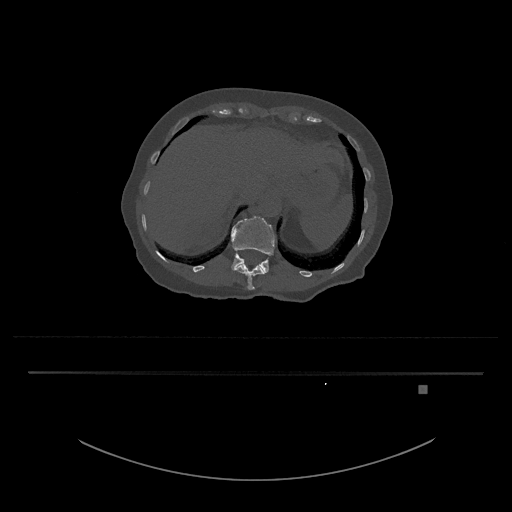
CT including the spine, one axial slice; position 582 of 797 along the scan axis; reconstruction kernel Br40s/3; 120 kVp; bone window (W 1800 / L 400 HU); 0.5 mm slice thickness; 512 × 512 image matrix, field of view 500 × 500 mm. Female patient, age 57 years. Case-level facts recorded for this patient, not image findings: primary cancer: cervical.
Outlined on this slice (semi-automatically segmented with operator editing):
- L1 vertebra: bounding box [x1, y1, x2, y2] px = [231, 216, 276, 273]
- T12 vertebra: [234, 262, 265, 290]